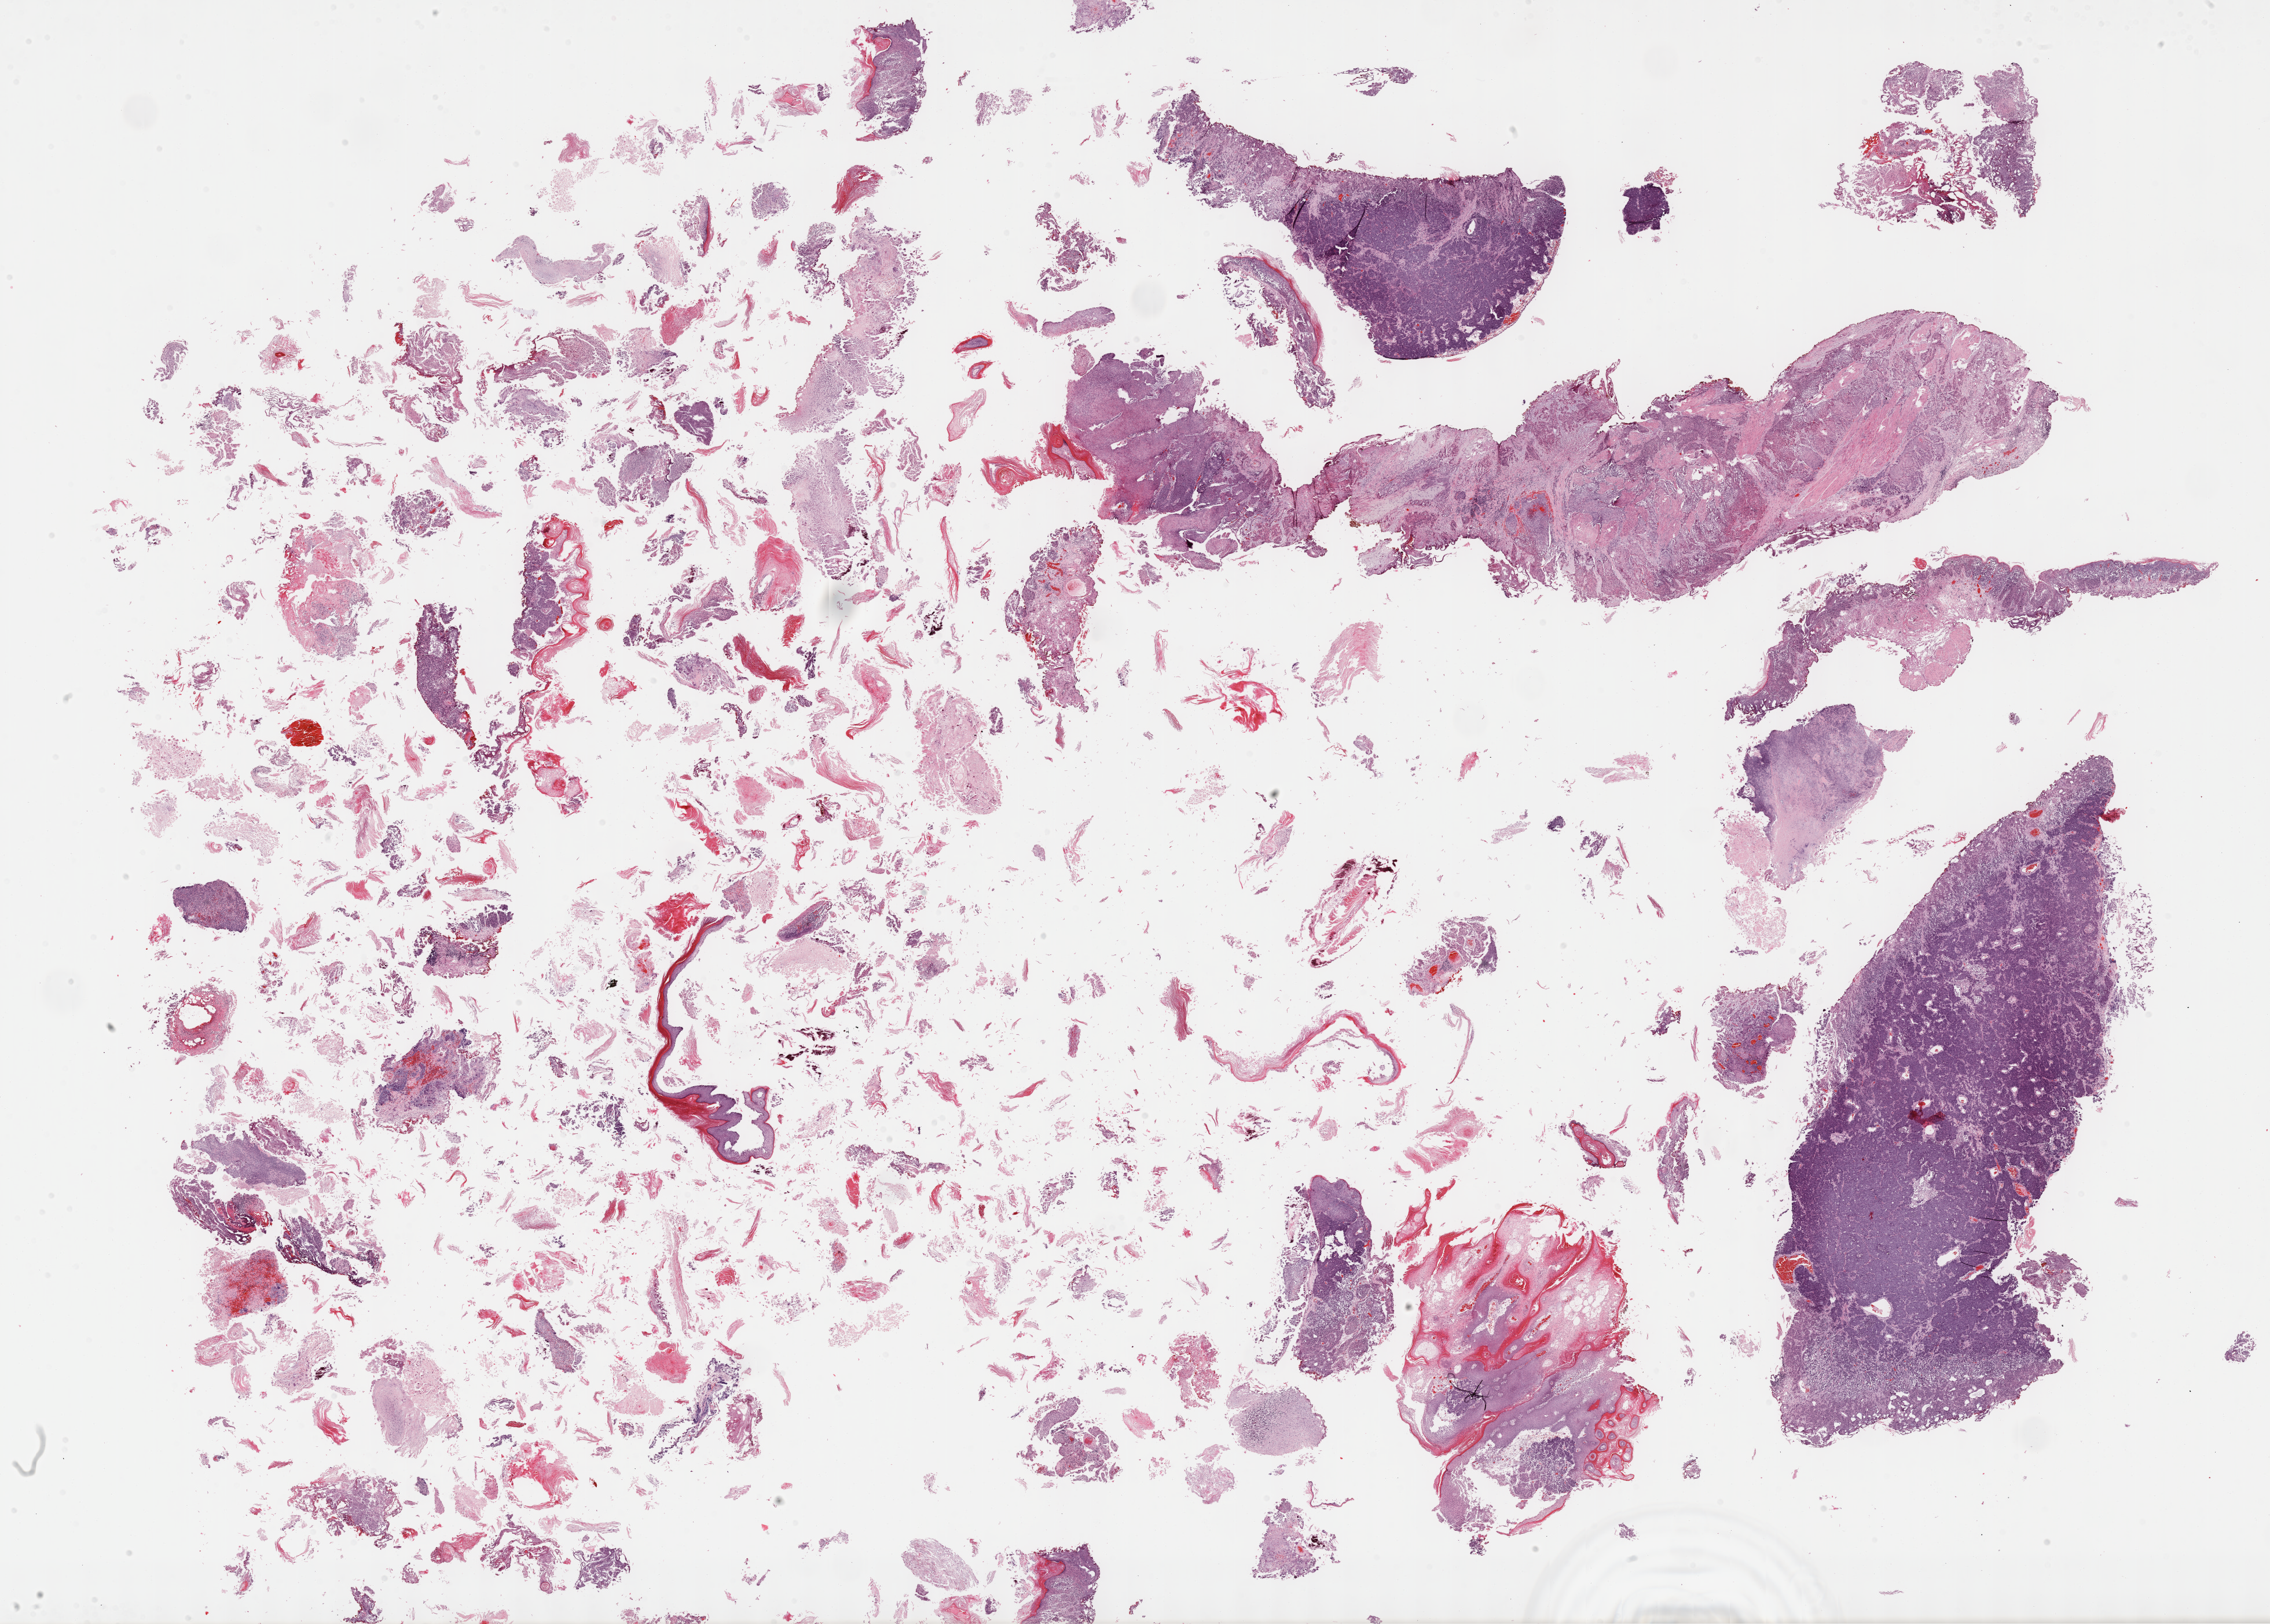
Digitized H&E-stained tissue section (whole slide) — low-resolution overview of the scanned area, about 31.7 x 22.7 mm. Formalin-fixed paraffin-embedded (FFPE) diagnostic section. Primary tumour sample from the bladder. Male, age 71 years at initial diagnosis. Histologic grade: high grade.
Pathologic diagnosis: Transitional cell carcinoma. AJCC pathologic stage: IV (7th edition).